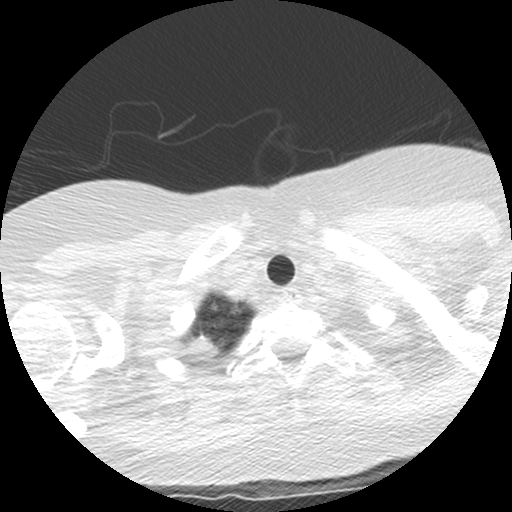
Low-dose screening chest CT, one axial slice. Slice 123 of 130 in the series (ordered by position). Reconstruction kernel STANDARD. 120 kVp. Lung window (W 1500 / L -600 HU). 2.5 mm slice thickness. 512 × 512 image matrix, field of view 290 × 290 mm.
Outlined on this slice (manually delineated by an expert):
- lesion 1 (tumor, upper lobe of right lung): box from (x=191, y=335) to (x=217, y=356) px